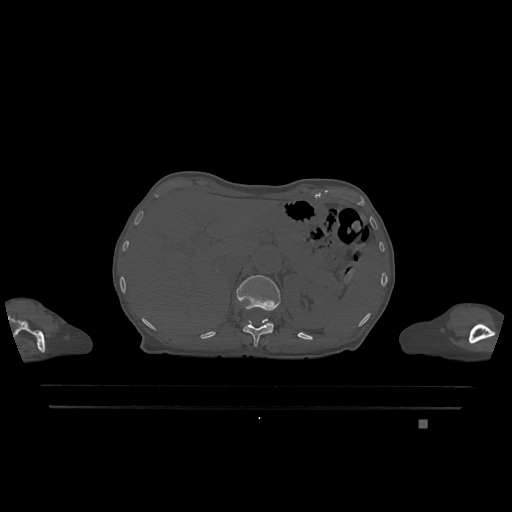
CT including the spine, one axial slice. Position 509 of 1317 along the scan axis. Bone window (W 1800 / L 400 HU). 512 × 512 image matrix. Female patient, age 74 years. Case-level facts recorded for this patient, not image findings: primary cancer: lung.
Outlined on this slice (semi-automatically segmented with operator editing):
- L1 vertebra: box from (x=236, y=275) to (x=281, y=332) px
- T12 vertebra: (x=243, y=319)–(x=272, y=347)